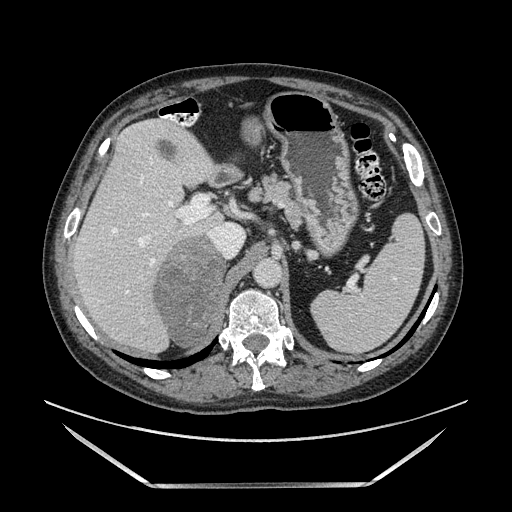
Contrast-enhanced abdominal CT, one axial slice. Position 98 of 185 along the scan axis. Soft-tissue window (W 400 / L 40 HU). 1.25 mm slice thickness. 512 × 512 image matrix. Male patient. From the clinical record (not read from this slice): diagnosis: adrenocortical carcinoma; tumour side: right adrenal; tumour size at pathology: 10.3 cm; Ki-67 index: 20 %; stage (as recorded): 3.
Annotated regions visible in this slice (semi-automatically segmented with operator editing):
- mass: bounding box <155,234,228,349> (left, top, right, bottom; pixels)